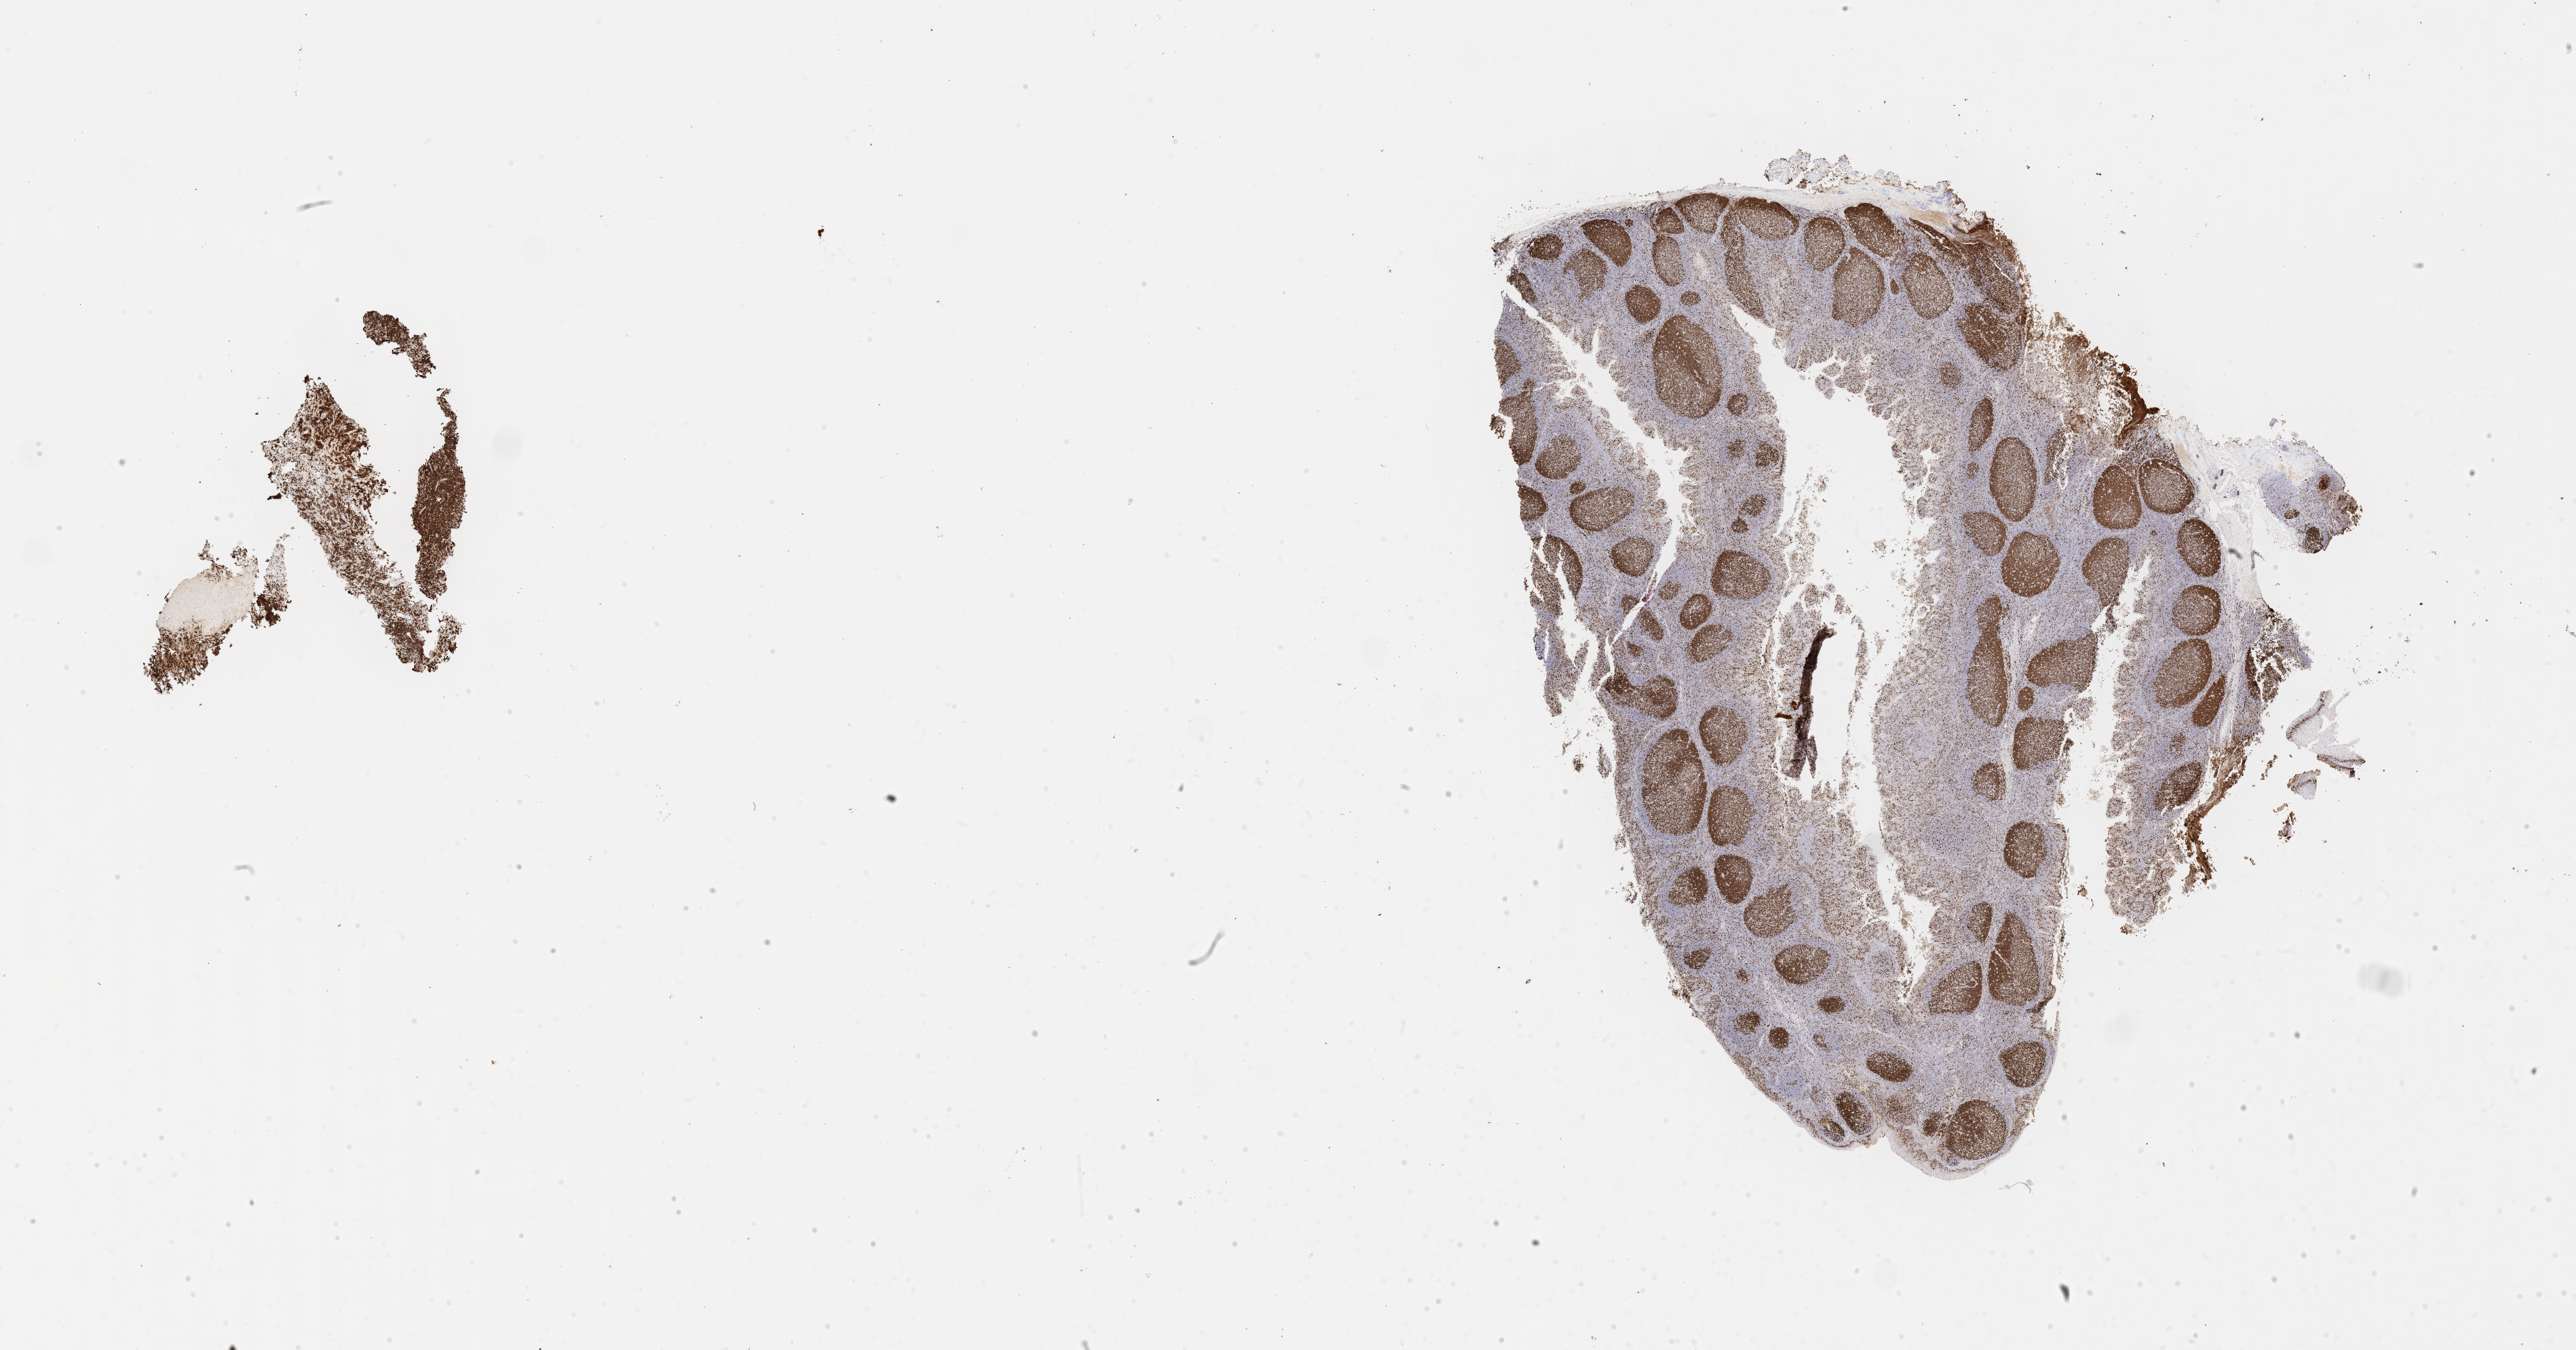
IHC for Ki-67, whole-slide image, shown as a low-resolution overview of the whole scanned area (about 30.7 x 16.1 mm). Tumor tissue. Anatomic site: pelvis. Patient: female, age at initial diagnosis 7 years.
* histologic diagnosis: Burkitt lymphoma, NOS